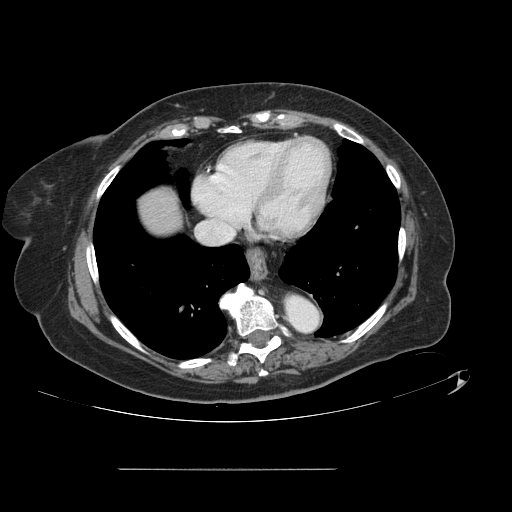
Contrast-enhanced abdominal CT, one axial slice; position 130 of 148 along the scan axis; 120 kVp; intravenous contrast given; soft-tissue window (W 400 / L 40 HU); 2.5 mm slice thickness; 512 × 512 image matrix. Female patient, age 75 years. Case-level facts recorded for this patient, not image findings: diagnosis: colorectal cancer liver metastases, imaged before liver resection; multiple liver metastases: no; largest metastasis: 2.4 cm; chemotherapy before resection: no.
Structures marked on this image (expert manual segmentation):
- liver: box from (x=139, y=190) to (x=181, y=234) px
- planned liver remnant (the part of the liver to remain after resection): (x=139, y=191)–(x=180, y=234)